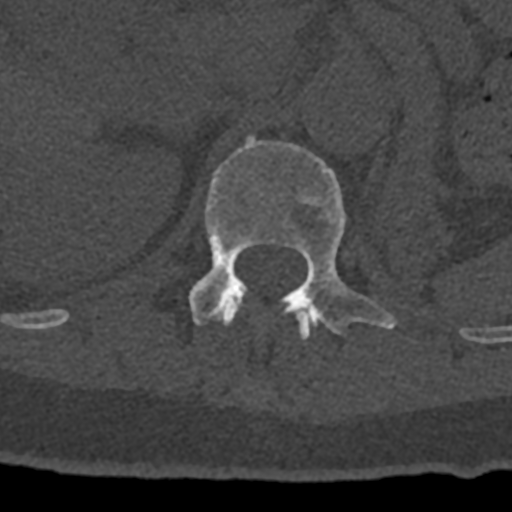
CT including the spine, one axial slice. Reconstruction kernel Br40s/3. Bone window (W 1800 / L 400 HU). 0.5 mm slice thickness. 512 × 512 image matrix, field of view 160 × 160 mm. Male patient, age 74 years. From the clinical record (not read from this slice): primary cancer: renal.
Annotated regions visible in this slice (semi-automatically segmented with operator editing):
- L1 vertebra: bounding box [x1, y1, x2, y2] px = [188, 136, 396, 334]
- T12 vertebra: [220, 298, 315, 339]